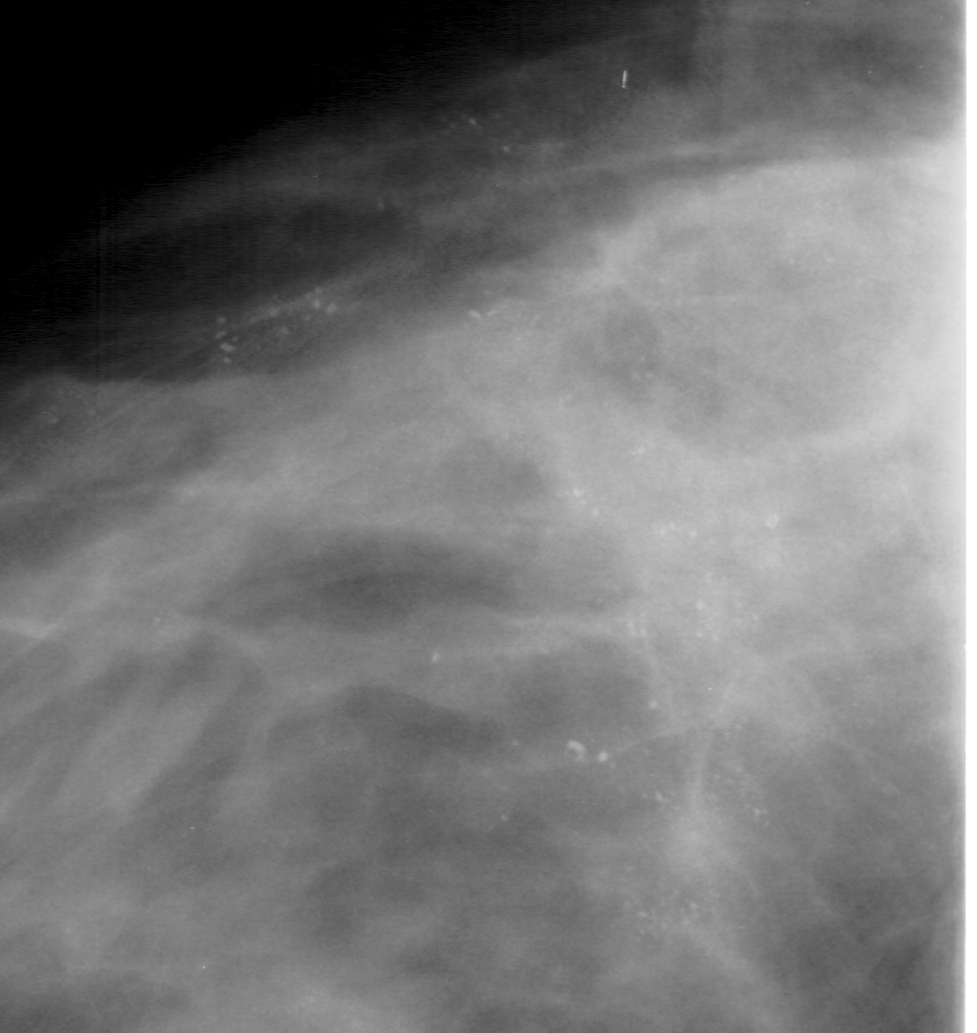
Cropped region of a digitized screen-film mammogram centred on a radiologist-marked abnormality; left breast; CC view; BI-RADS breast density category 4 (scale 1–4).
Calcifications, morphology pleomorphic, distribution segmental; BI-RADS assessment category 5; subtlety rating 4 on a 1 (subtle) to 5 (obvious) scale; pathology (as recorded): malignant.